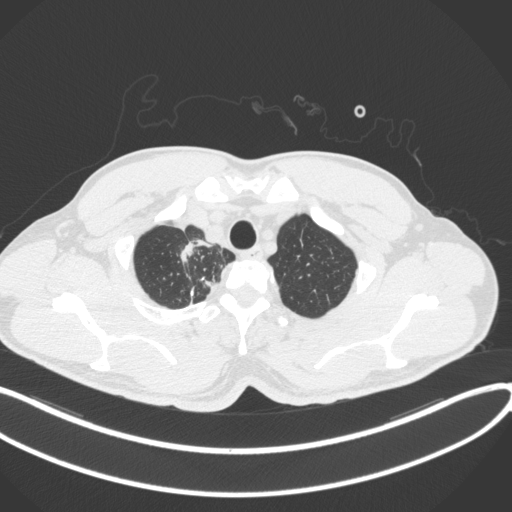
Chest CT, one axial slice; position 336 of 391 along the scan axis; reconstruction kernel B31f; 120 kVp; lung window (W 1500 / L -600 HU); 512 × 512 image matrix, field of view 400 × 400 mm. Male patient, age 48 years. From the clinical record (not read from this slice): clinical TNM (as recorded): T1c N1 M1.
Outlined on this slice (bounding box drawn by a radiologist):
- lung tumour (recorded histology: adenocarcinoma): box from (x=180, y=239) to (x=201, y=265) px